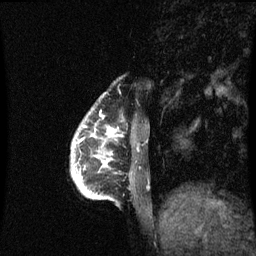
Breast MRI (dynamic contrast-enhanced), one sagittal slice; dynamic contrast-enhanced series, image 2 of 3 at this slice position (ordered by acquisition); 1.5 T; TE 4.2 ms, TR 8.9 ms; 2 mm slice thickness; 256 × 256 image matrix, field of view 200 × 200 mm. Patient: female, 35 years. Case-level facts recorded for this patient, not image findings: setting: breast cancer imaged before/during neoadjuvant chemotherapy; receptor status: HR-positive, HER2-negative.
Annotated regions visible in this slice (semi-automatically segmented with operator editing):
- analysis volume of interest (the breast-tissue region the enhancement analysis was run in; not a lesion): bounding box <71,122,115,199> (left, top, right, bottom; pixels)
- tumour enhancement mask (voxels above the 70 % enhancement threshold inside the analysis volume of interest): <80,162,107,187>